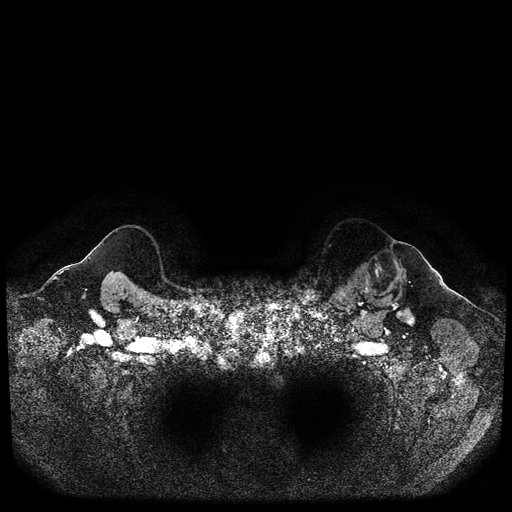
Breast MRI (dynamic contrast-enhanced, multi-phase), one axial slice; slice 94 of 116 in the series (ordered by position); dynamic contrast-enhanced series, time point 2 of 5 at this slice position (early post-contrast); 1.5 T; TE 2.6 ms, TR 5.3 ms; 512 × 512 image matrix, field of view 350 × 350 mm. Female patient, age 64 years.
Outlined on this slice (semi-automatic segmentation, software-assisted and operator-edited):
- breast lesion (labelled 'tumour' in the annotation; benign lesions carry a separate 'benign' label): box from (x=356, y=248) to (x=411, y=313) px